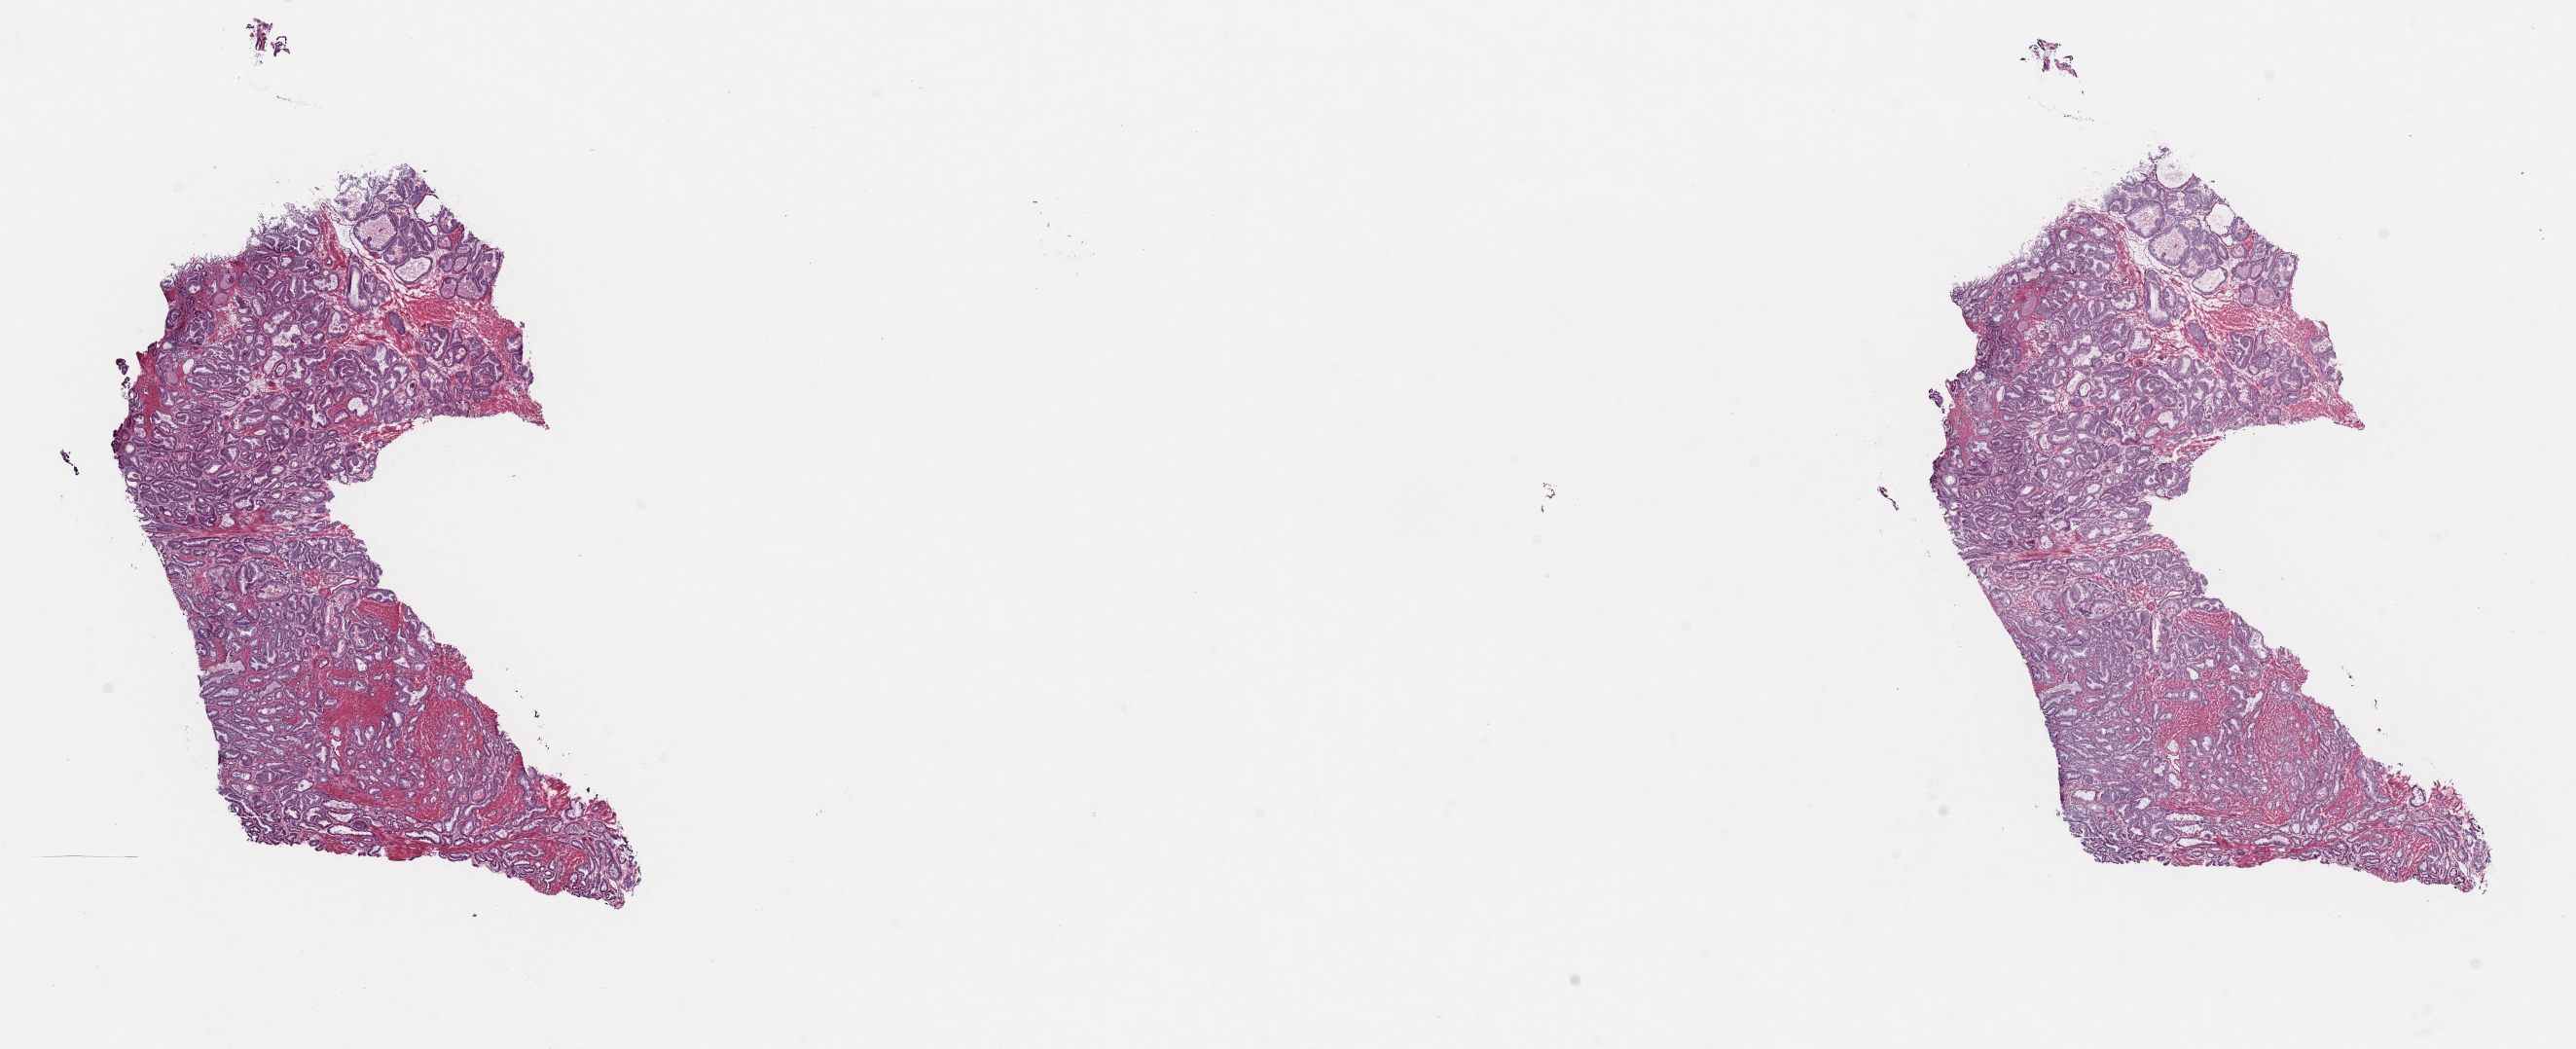
Digitized Hematoxylin and eosin (H&E) stained tissue section (whole slide) — shown as a low-resolution overview of the whole scanned area (about 20.9 x 8.5 mm, slide scanned at 40x), frozen section from the top of the tissue portion, prostate, primary tumour sample. Male patient; age at initial diagnosis 57 years. Gleason score: 8 (3+5). Slide review estimates, as recorded: tumour cells 75%, tumour nuclei 95%, normal cells 0%, stromal cells 25%, necrosis 0%. Infiltration values recorded for this section: lymphocyte infiltration 1%, monocyte infiltration 1%, neutrophil infiltration 0%.
Laterality: bilateral. Histologic diagnosis: Adenocarcinoma, NOS (prostate gland). Lymph nodes positive (case pathology): 0 of 24 examined.